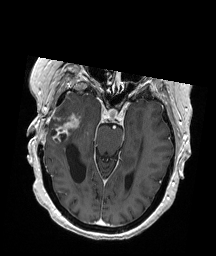
Brain MRI from a brain-tumour surgery series, one axial slice; position 123 of 192 along the scan axis; T1-weighted post-contrast; 1 mm slice thickness; 216 × 256 image matrix. Case-level facts recorded for this patient, not image findings: histopathology: Glioblastoma; WHO grade: 4; IDH mutation: no; tumour location: Right Temporal.
Structures marked on this image (manually delineated by an expert):
- tumour: bounding box <50,114,81,132> (left, top, right, bottom; pixels)